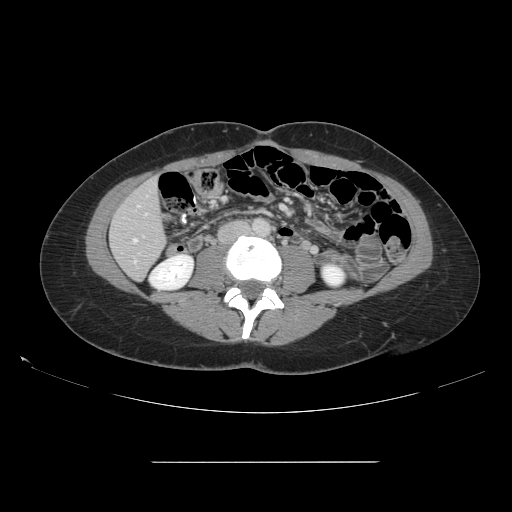
Contrast-enhanced abdominal CT, one axial slice; position 34 of 151 along the scan axis; 120 kVp; intravenous contrast given; soft-tissue window (W 400 / L 40 HU); 512 × 512 image matrix, field of view 421 × 421 mm. Female patient, age 46 years. From the clinical record (not read from this slice): diagnosis: colorectal cancer liver metastases, imaged before liver resection; multiple liver metastases: yes; largest metastasis: 3 cm; disease in both lobes: yes.
Structures marked on this image (manually delineated by an expert):
- hepatic veins: bounding box (x1, y1, x2, y2) in pixels: (134, 239, 136, 242)
- liver: (111, 179, 166, 280)
- planned liver remnant (the part of the liver to remain after resection): (111, 179, 166, 280)